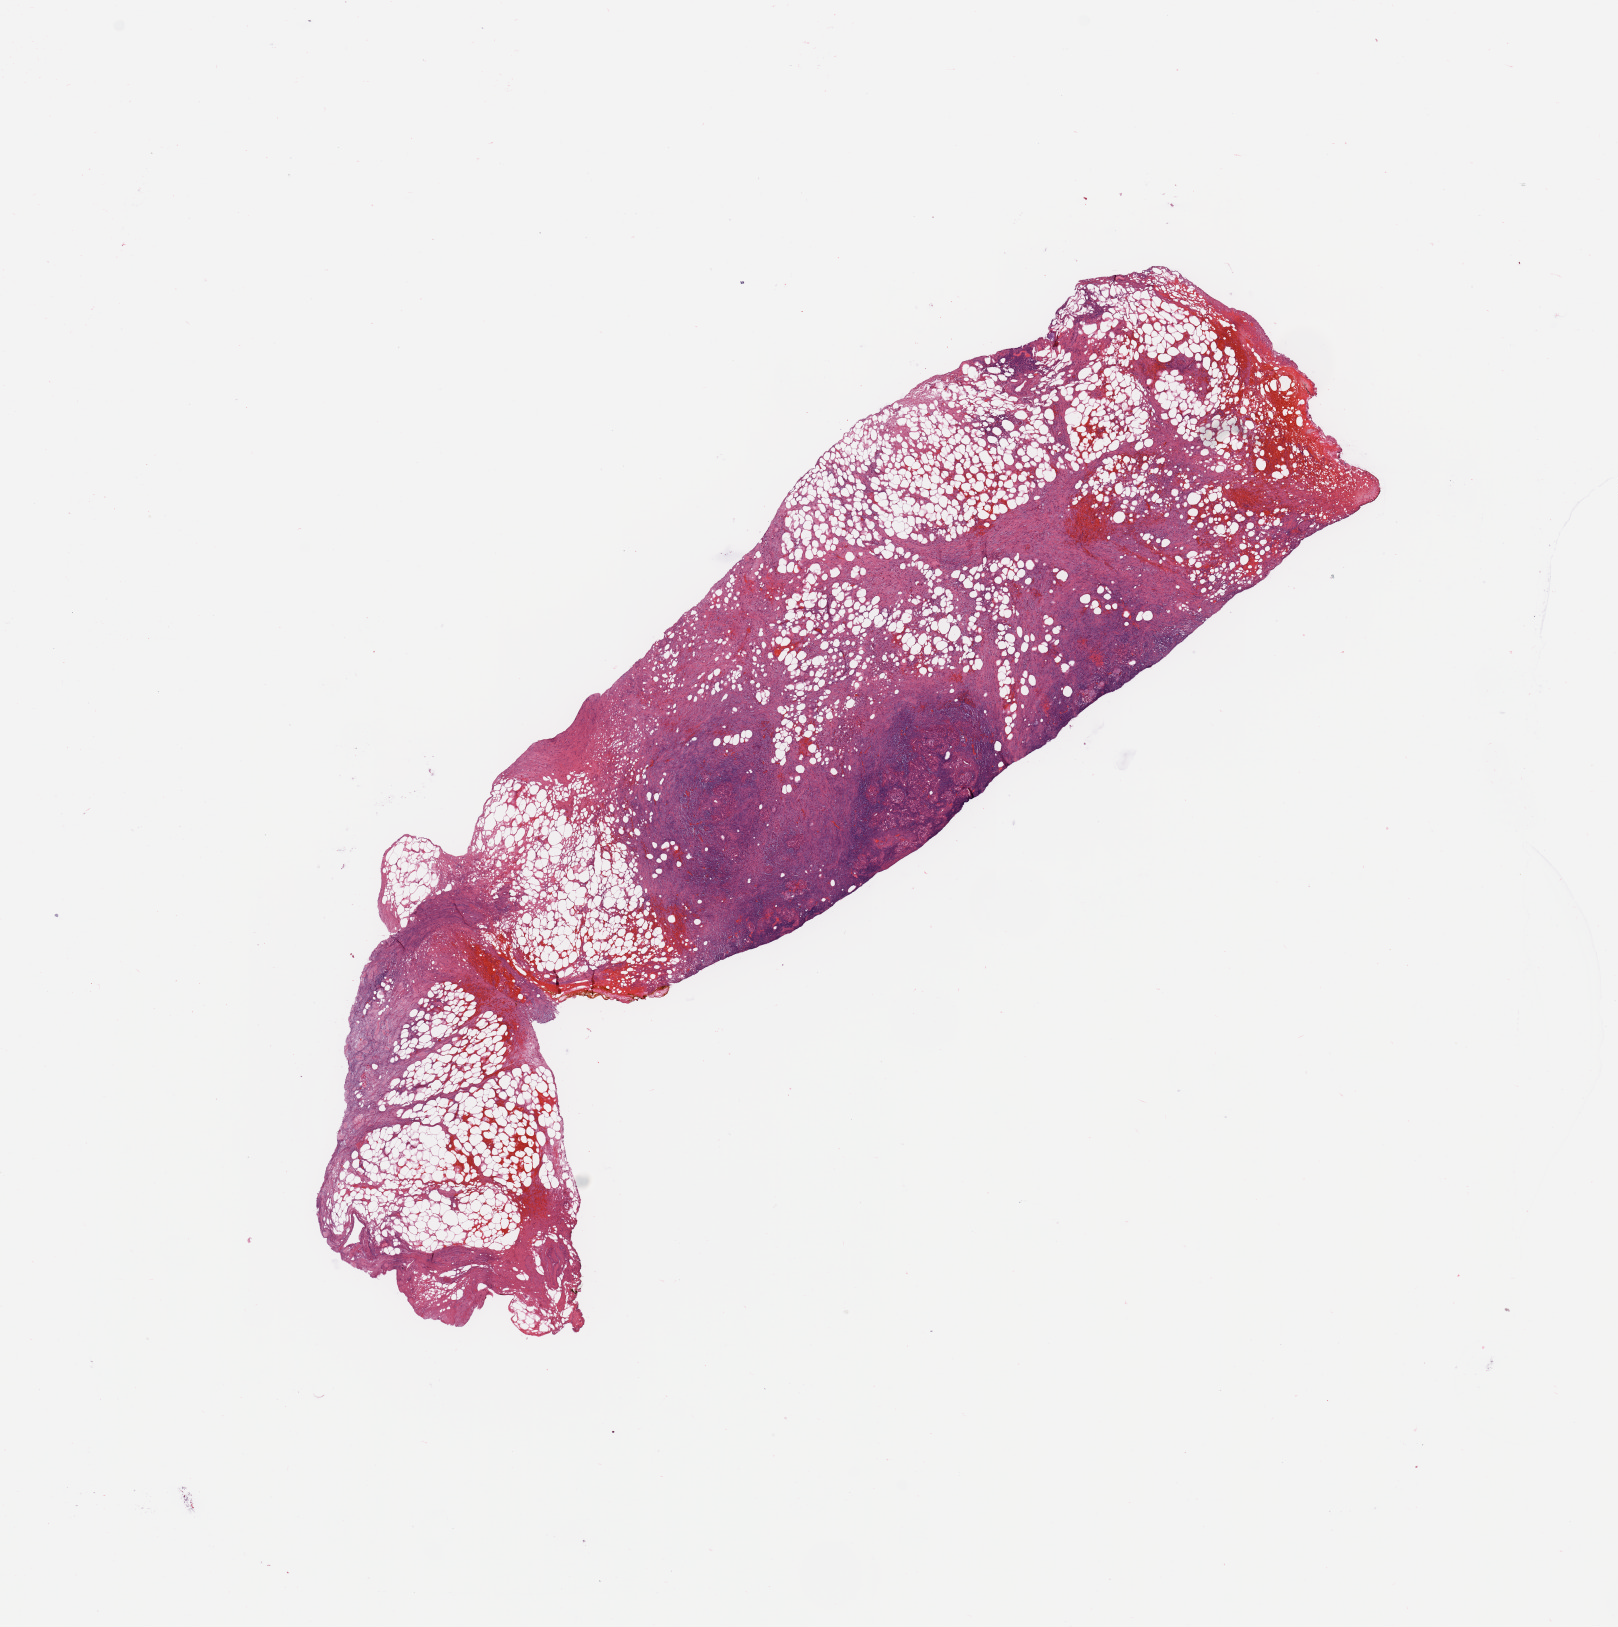
Hematoxylin and eosin (H&E) stained whole-slide image, shown as a low-resolution overview of the whole scanned area (about 12.8 x 12.9 mm), pancreas, normal (non-tumour) tissue. 71-year-old male patient.
* this section: normal (non-tumour) tissue from the same patient
* patient diagnosis: Infiltrating duct carcinoma, NOS